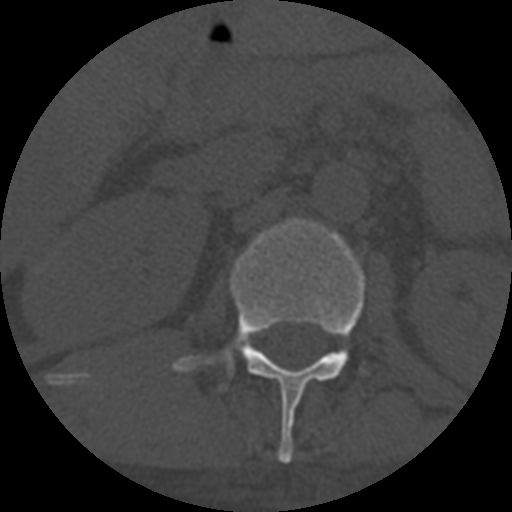
CT including the spine, one axial slice. Position 285 of 708 along the scan axis. Reconstruction kernel STANDARD. One of 3 acquisitions stored at this slice position. Bone window (W 1800 / L 400 HU). 1.25 mm slice thickness. 512 × 512 image matrix, field of view 160 × 160 mm. Patient age 55 years. Case-level facts recorded for this patient, not image findings: primary cancer: colon.
Annotated regions visible in this slice (semi-automatic segmentation, software-assisted and operator-edited):
- L1 vertebra: bounding box (x1, y1, x2, y2) in pixels: (172, 219, 365, 464)